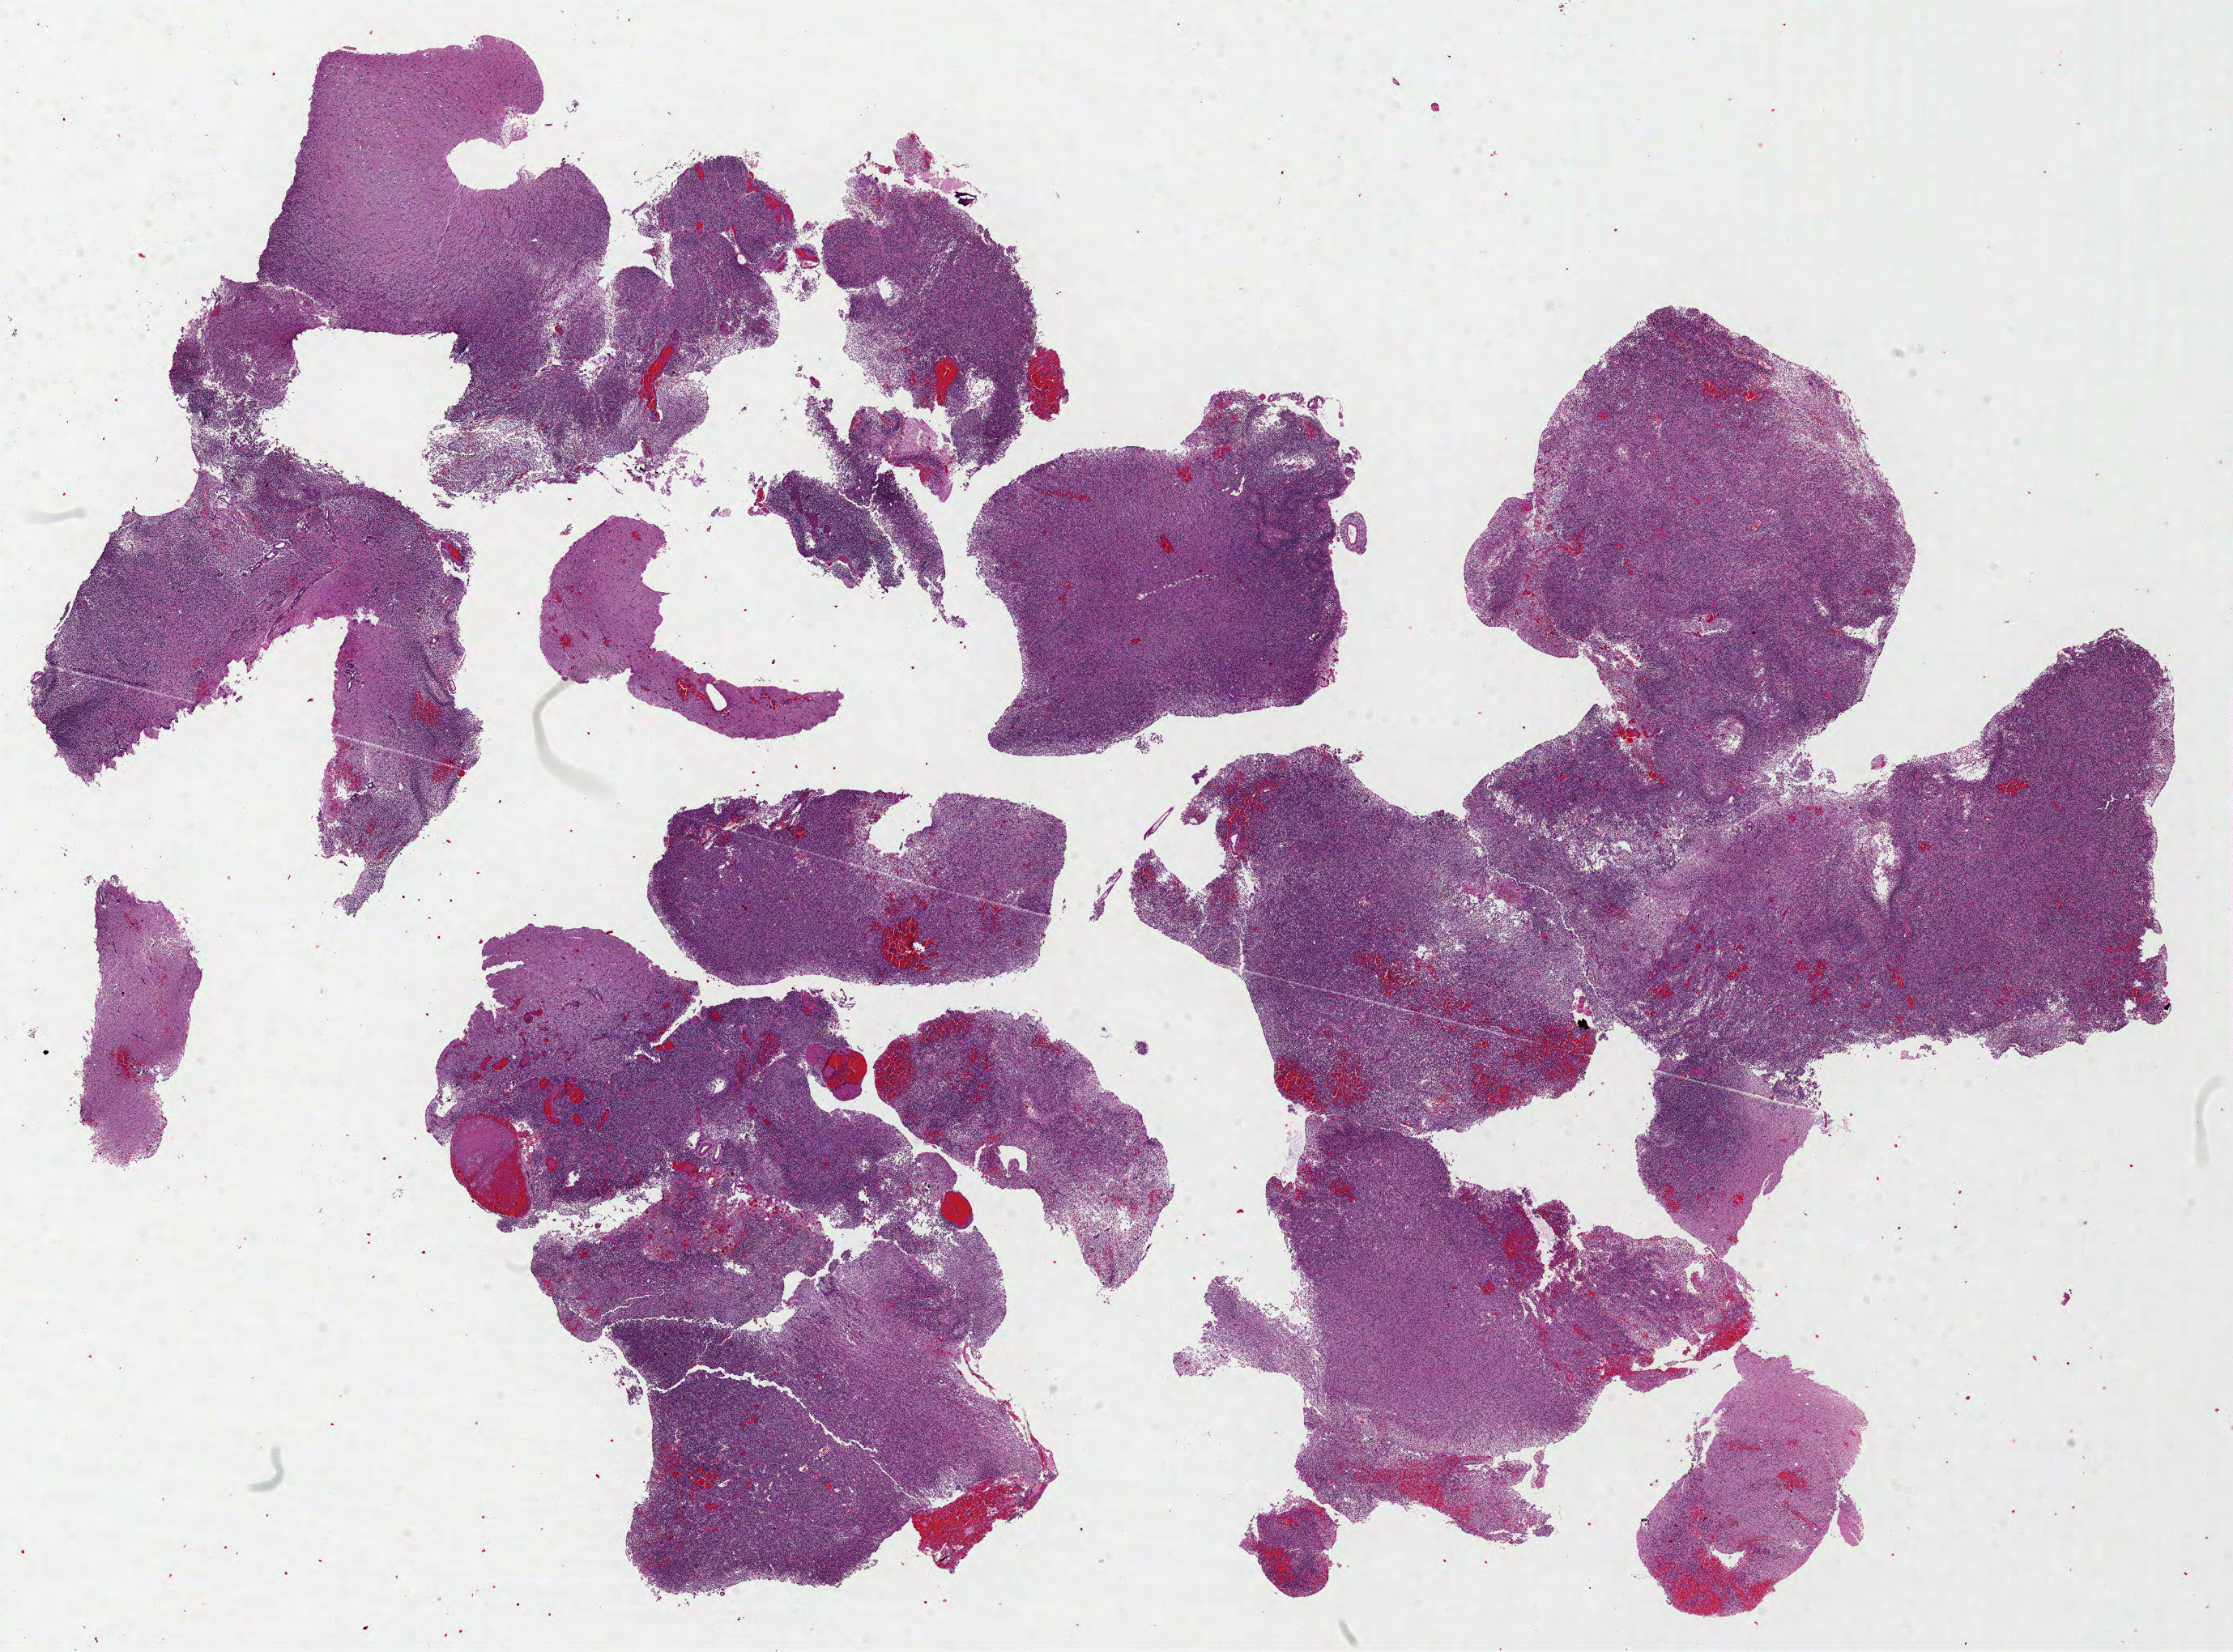
Whole-slide histology image, Hematoxylin and eosin (H&E) stained, whole scanned area (about 22.2 x 16.5 mm, slide scanned at 40x) shown as a low-resolution overview, formalin-fixed paraffin-embedded (FFPE) diagnostic section, primary tumour sample from the brain. Female patient; age at initial diagnosis 55 years.
* histologic diagnosis: Glioblastoma